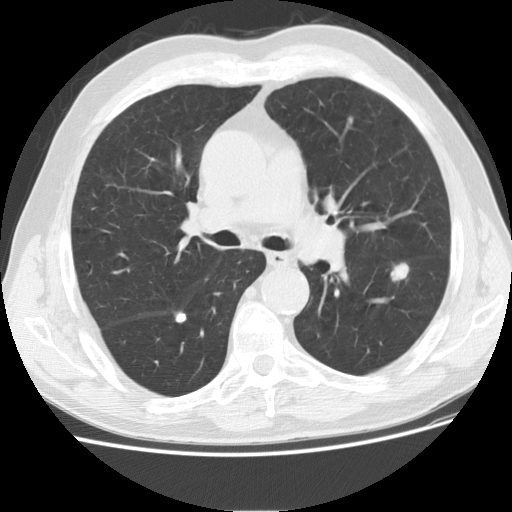
Axial slice from a low-dose chest CT screening exam. Second annual screen. Lung window (W 1500 / L -600 HU). Male participant, aged 73 years at enrolment. Current smoker at enrolment.
- Expert reader's lesion annotation, bounding box [x1, y1, x2, y2] px = [368, 254, 424, 300].
- Reader record for this screening exam (exam-level; its link to the box is not recorded): non-calcified nodule or mass ≥4 mm, left lower lobe, 16 × 10 mm, smooth margins, soft tissue attenuation, pre-existing on the prior screen: yes; interval growth: yes.
- Participant outcome: lung cancer diagnosed 76 days after this screen — adenocarcinoma, NOS, left lower lobe, poorly differentiated (G3), stage IIA (AJCC 6th edition), 12 mm at pathology.